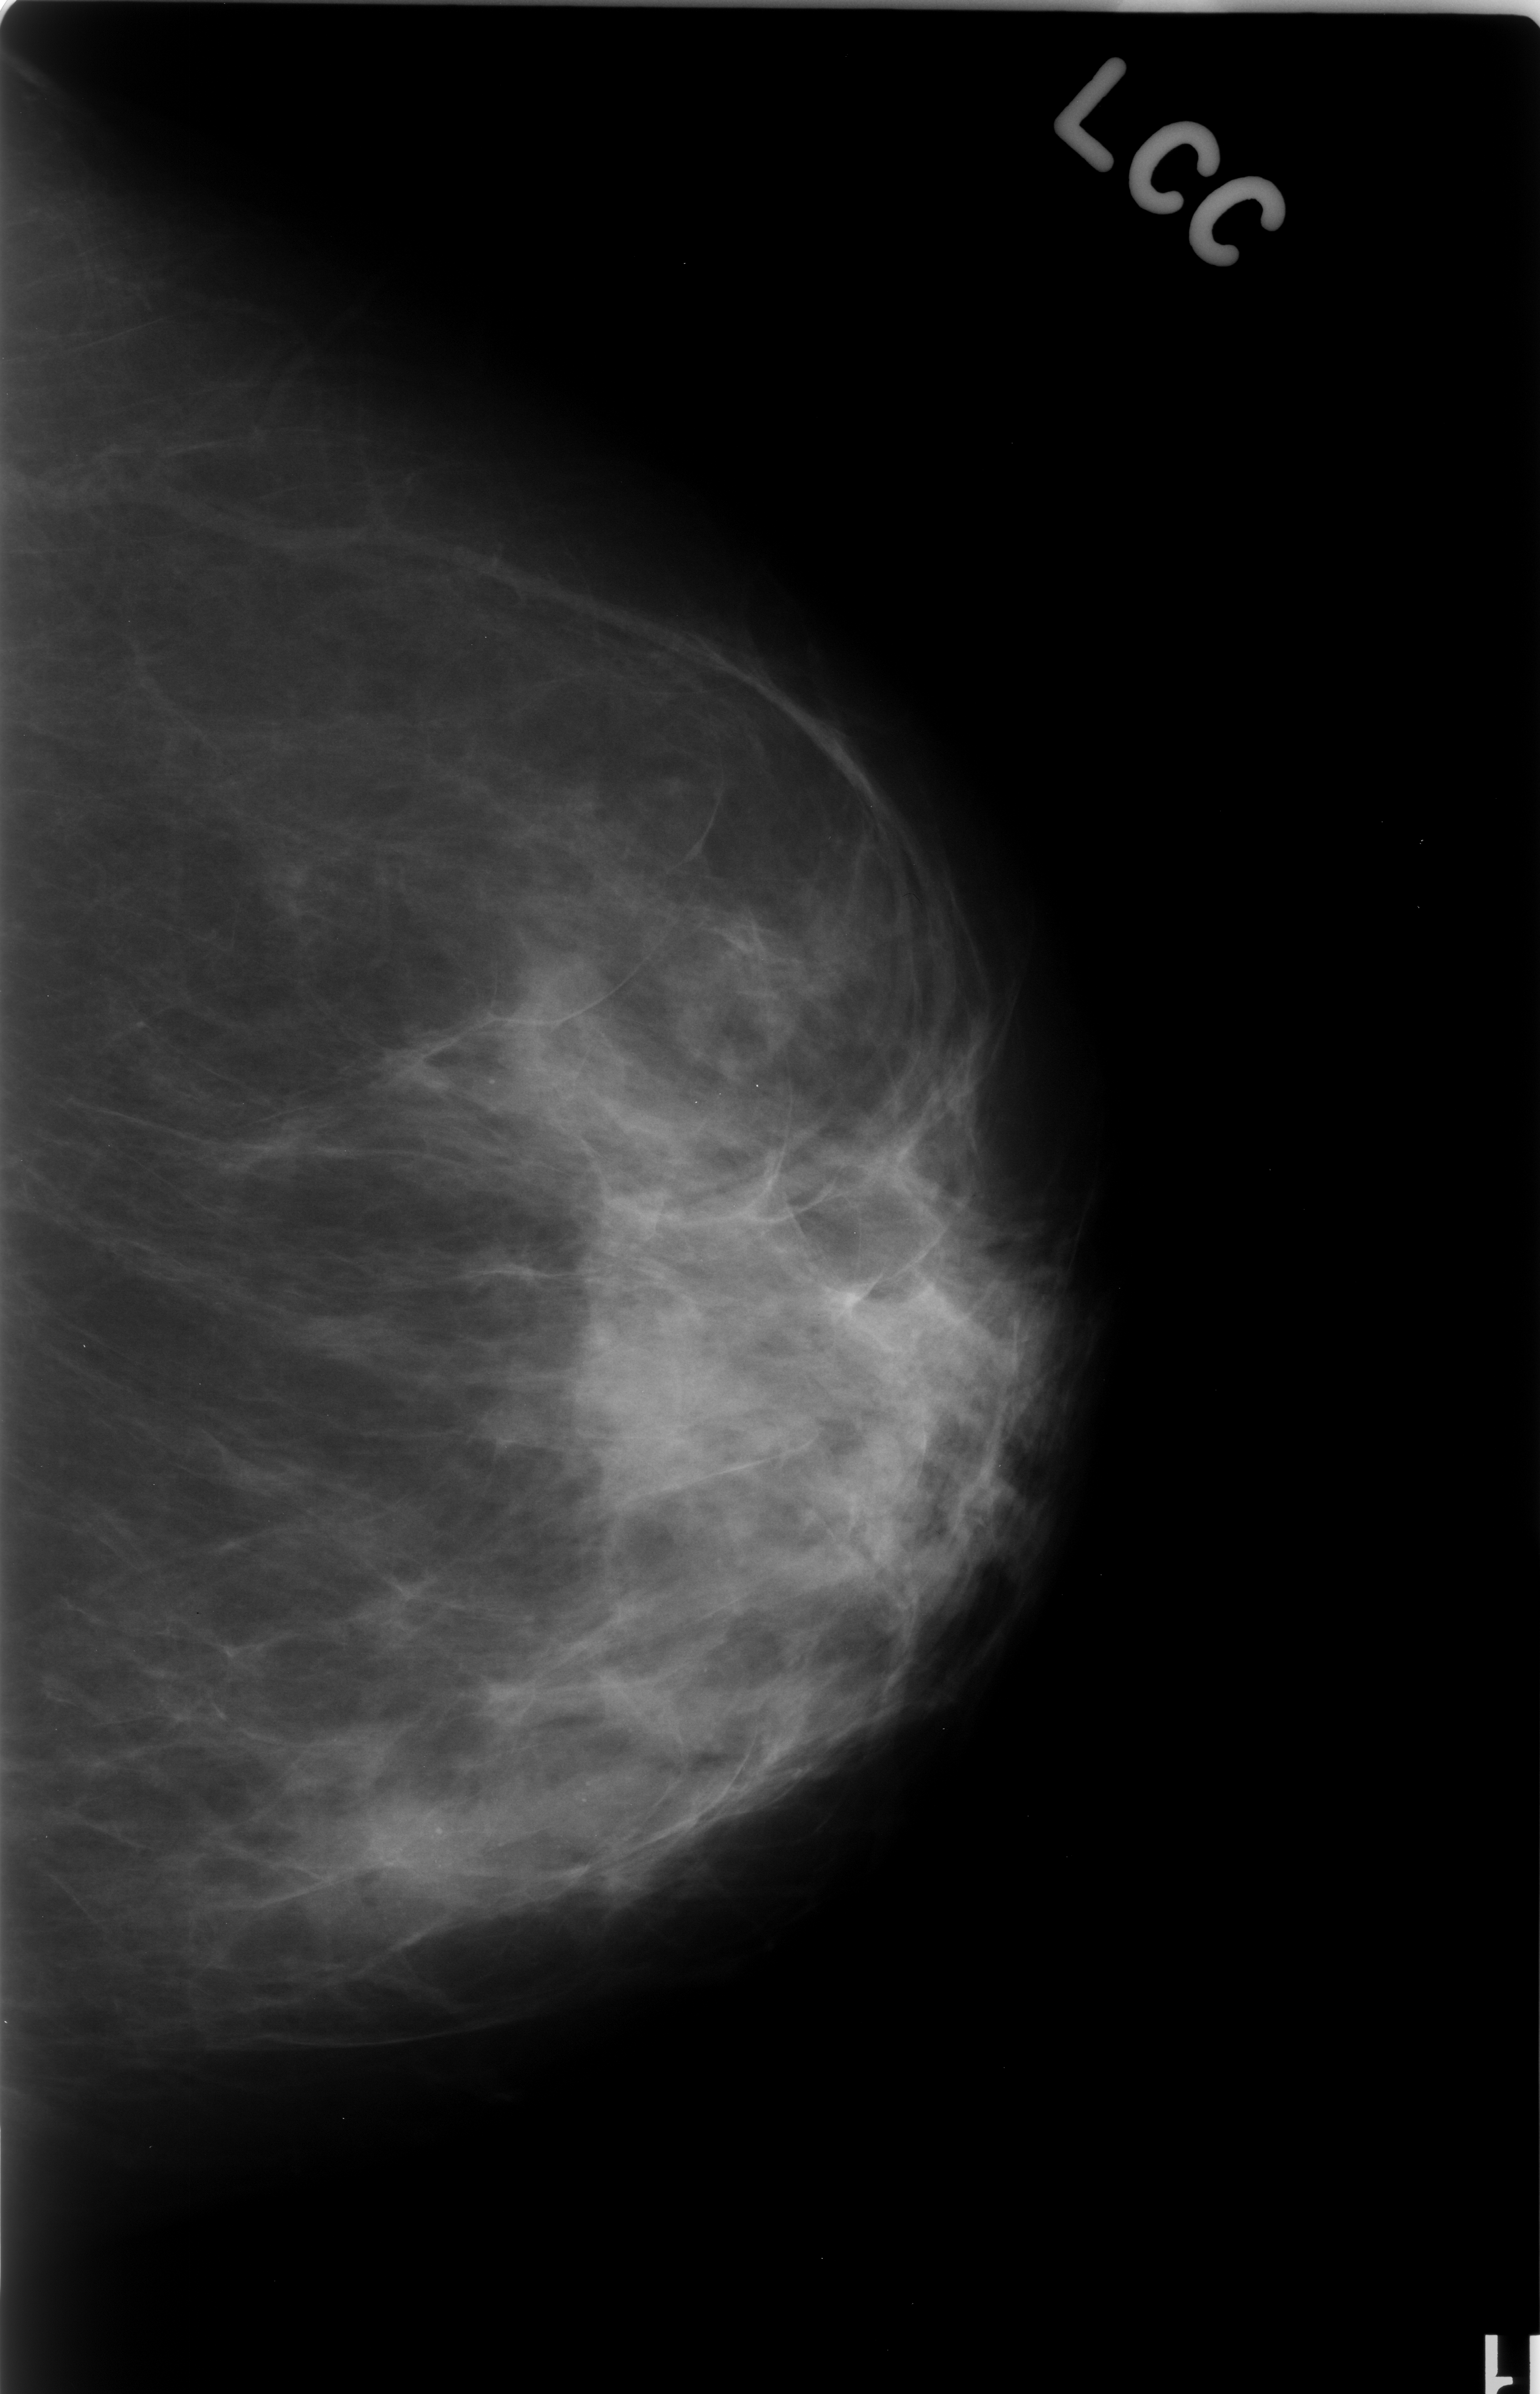
Scanned film-screen mammogram; left breast; craniocaudal (CC) view; breast composition: scattered fibroglandular densities (BI-RADS density category 2 of 4); 1540 × 2394 image matrix.
Expert-marked regions of interest on this film, with their recorded descriptors:
- calcifications, morphology amorphous, distribution segmental; BI-RADS assessment category 4; pathology (as recorded): benign: box from (x=315, y=1720) to (x=683, y=1924) px